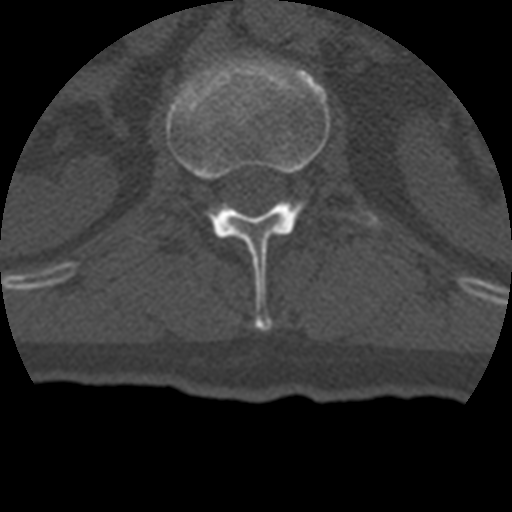
CT including the spine, one axial slice; position 141 of 399 along the scan axis; reconstruction kernel STANDARD; bone window (W 1800 / L 400 HU); 1.25 mm slice thickness; 512 × 512 image matrix, field of view 160 × 160 mm. Patient age 69 years. From the clinical record (not read from this slice): primary cancer: prostate.
Outlined on this slice (semi-automatically segmented with operator editing):
- L1 vertebra: bounding box (x1, y1, x2, y2) in pixels: (166, 55, 380, 331)